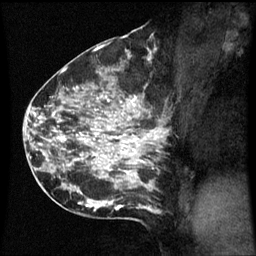
Breast MRI (dynamic contrast-enhanced), one sagittal slice. Position 34 of 60 along the scan axis. Dynamic contrast-enhanced series, image 2 of 3 at this slice position (ordered by acquisition). 1.5 T. TE 4.2 ms, TR 8.9 ms. 2.1 mm slice thickness. 256 × 256 image matrix. Patient: female, 42 years. From the clinical record (not read from this slice): setting: breast cancer imaged before/during neoadjuvant chemotherapy; receptor status: HER2-positive.
Outlined on this slice (semi-automatically segmented with operator editing):
- analysis volume of interest (the breast-tissue region the enhancement analysis was run in; not a lesion): bounding box <66,82,169,193> (left, top, right, bottom; pixels)
- tumour enhancement mask (voxels above the 70 % enhancement threshold inside the analysis volume of interest): <80,96,161,181>